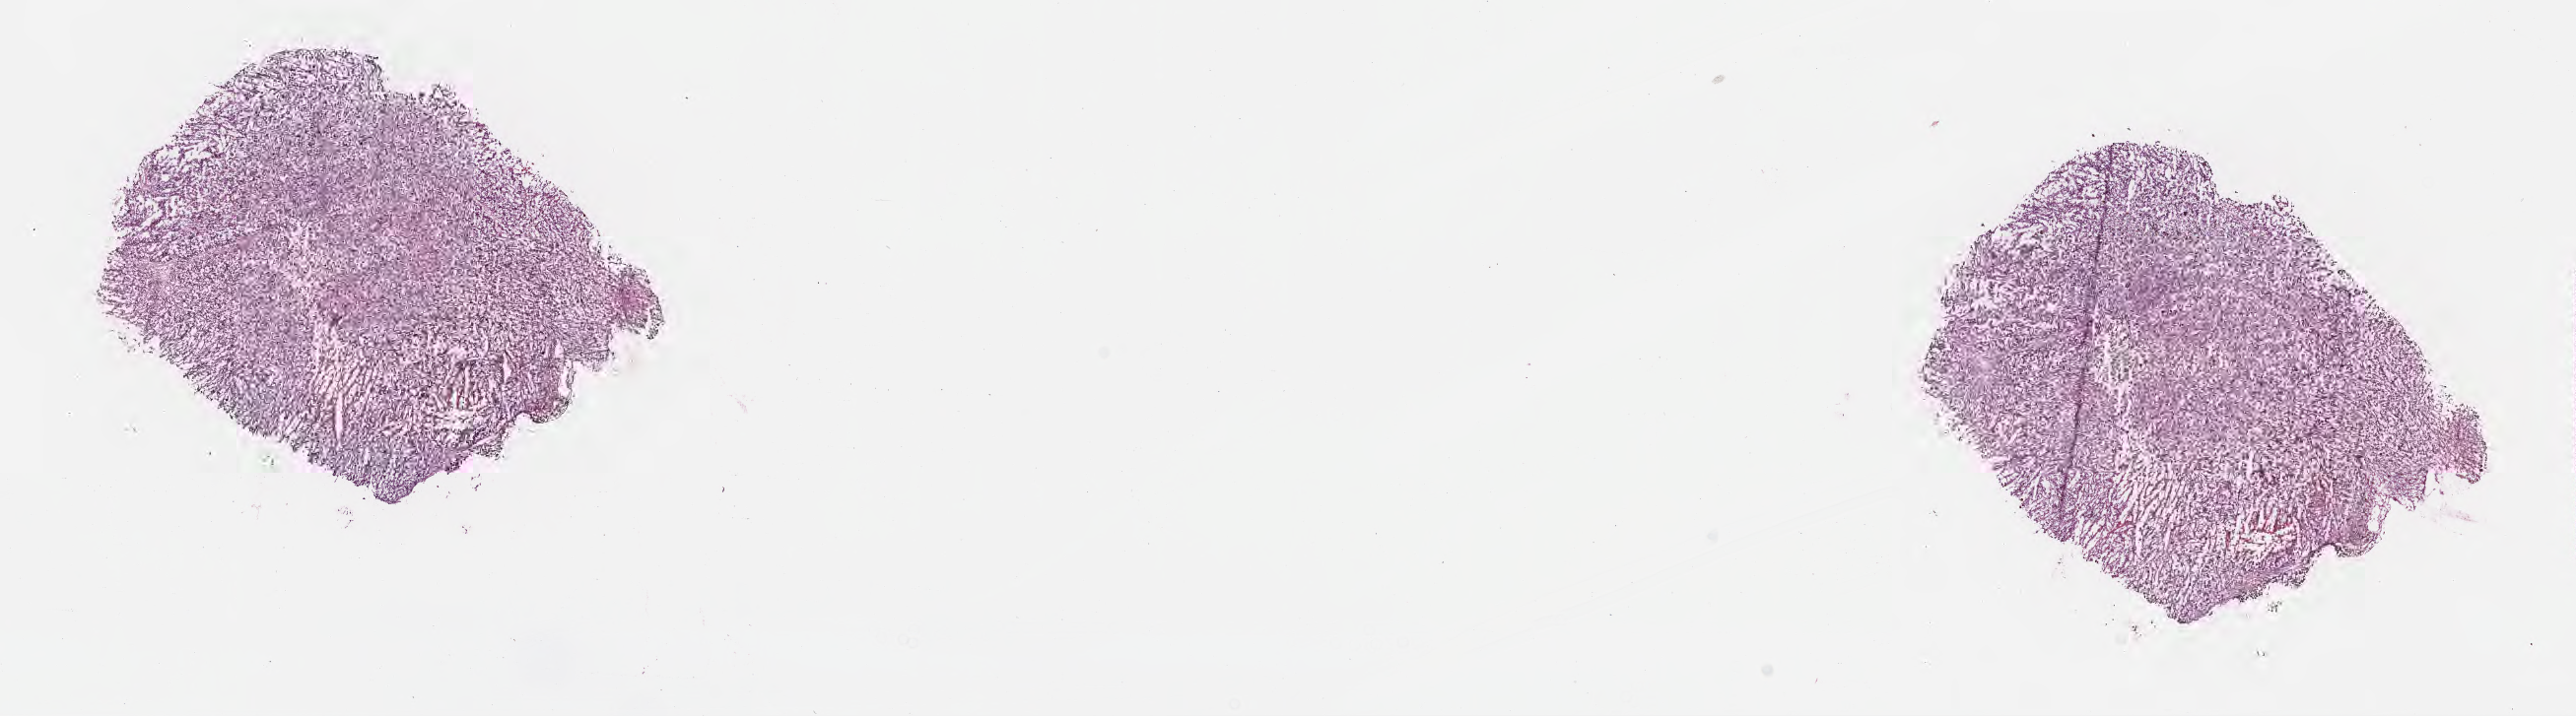
Digitized haematoxylin and eosin-stained section — low-resolution overview of the scanned area, about 21.1 x 5.9 mm, frozen section, specimen: metastatic tumor tissue, resected from lymph node. Male patient; age at initial diagnosis 74 years. Pathologist review of this section (percent, as recorded): tumor cells 81%, tumor nuclei 85%, stromal cells 2%, necrosis 3%, normal cells 14%. Inflammatory infiltration, as recorded: lymphocyte infiltration 1%, monocyte infiltration 8%, neutrophil infiltration 0%.
Section: top of the tissue portion. Patient diagnosis (primary): Malignant melanoma, NOS.